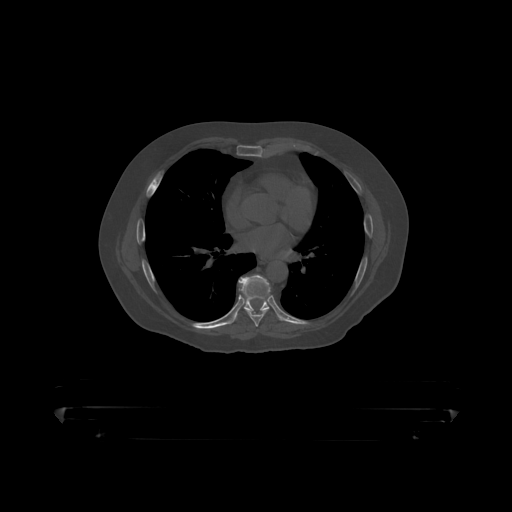
CT including the spine, one axial slice; position 269 of 390 along the scan axis; reconstruction kernel STANDARD; bone window (W 1800 / L 400 HU); 1.25 mm slice thickness; 512 × 512 image matrix, field of view 650 × 650 mm. Male patient, age 60 years. Case-level facts recorded for this patient, not image findings: primary cancer: prostate.
Outlined on this slice (semi-automatic segmentation, software-assisted and operator-edited):
- T7 vertebra: bounding box <240,290,268,319> (left, top, right, bottom; pixels)
- T8 vertebra: <235,275,271,316>